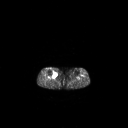
FDG PET of an extremity soft-tissue mass (from a PET/CT study), one axial slice; slice 149 of 267 in the series (ordered by position); 128 × 128 image matrix, field of view 700 × 700 mm. Patient: female, 65 years. From the clinical record (not read from this slice): histological type: undifferentiated – high grade; grade: high; site of the primary tumour: right thigh.
Outlined on this slice (expert contour drawn on MRI and transferred to this co-registered scan by the dataset authors):
- gross tumour volume (mass): bounding box (x1, y1, x2, y2) in pixels: (52, 71, 57, 77)